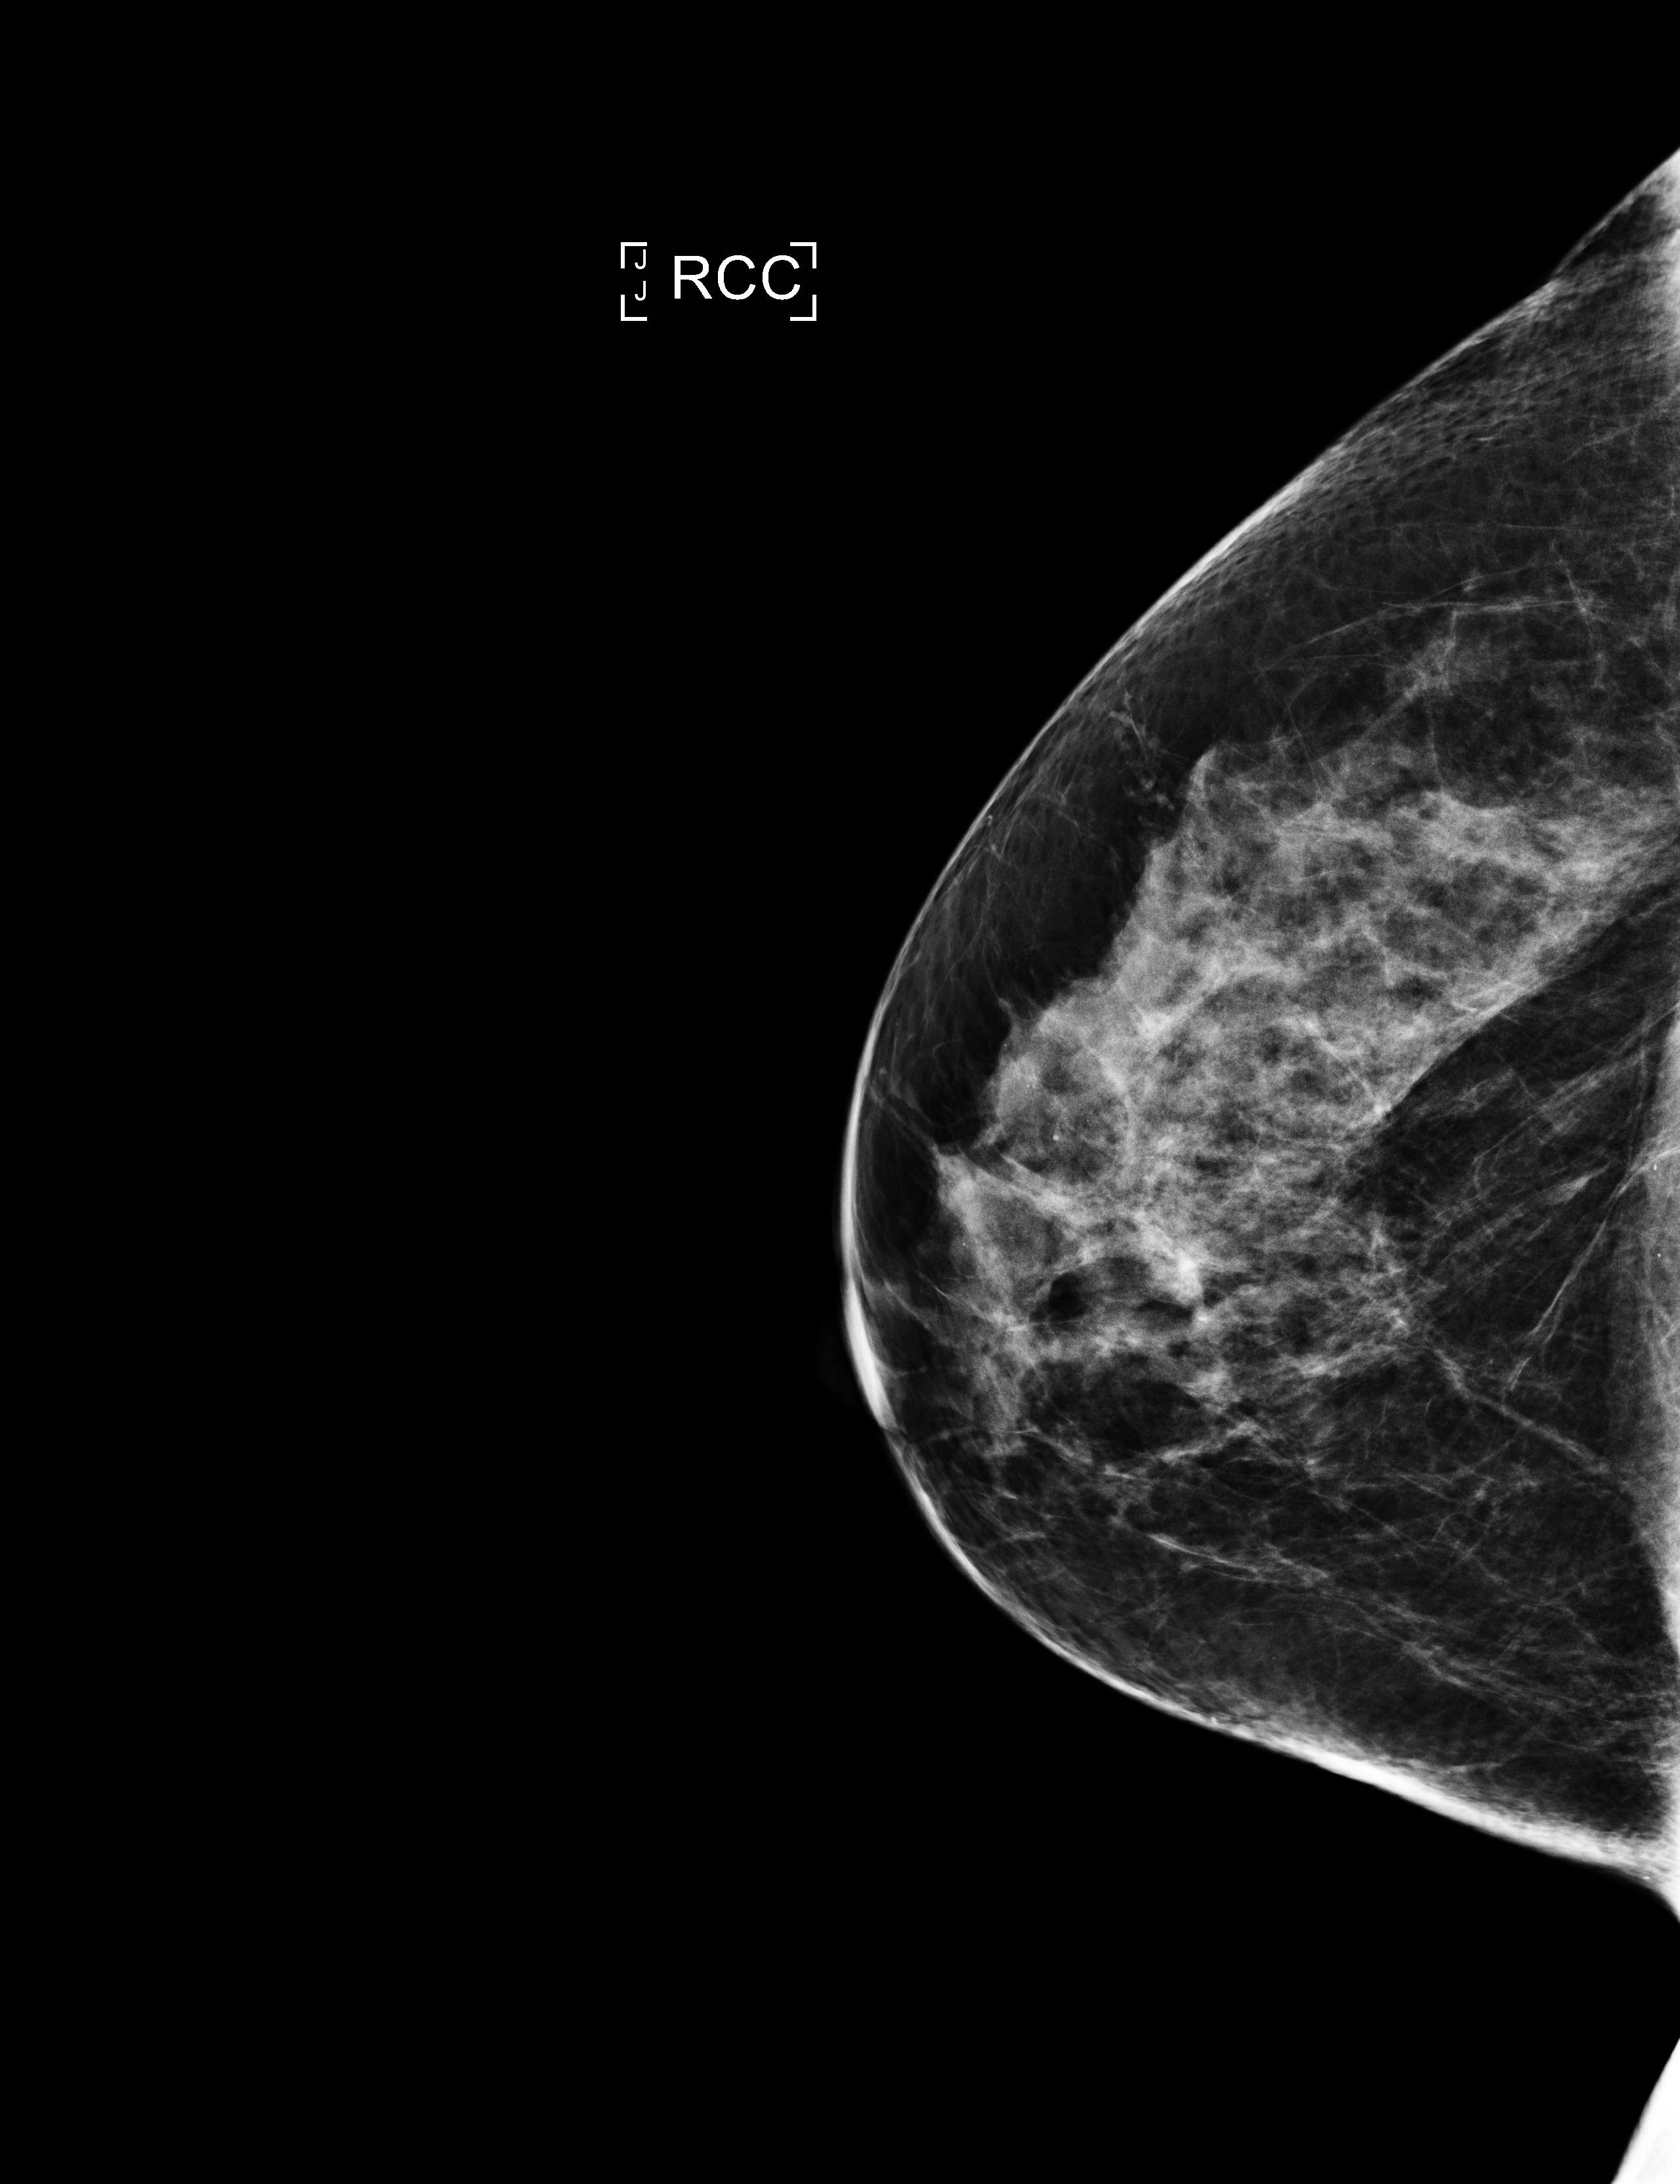
Full-field digital mammogram (FFDM), right breast, CC view, screening examination. Patient: female, 55 years.
- breast density at the screening exam (both breasts): heterogeneously dense (BI-RADS density category c)
- final BI-RADS category for the screening round (tomosynthesis exam, both breasts): category 2
- recall: no recall after this screen